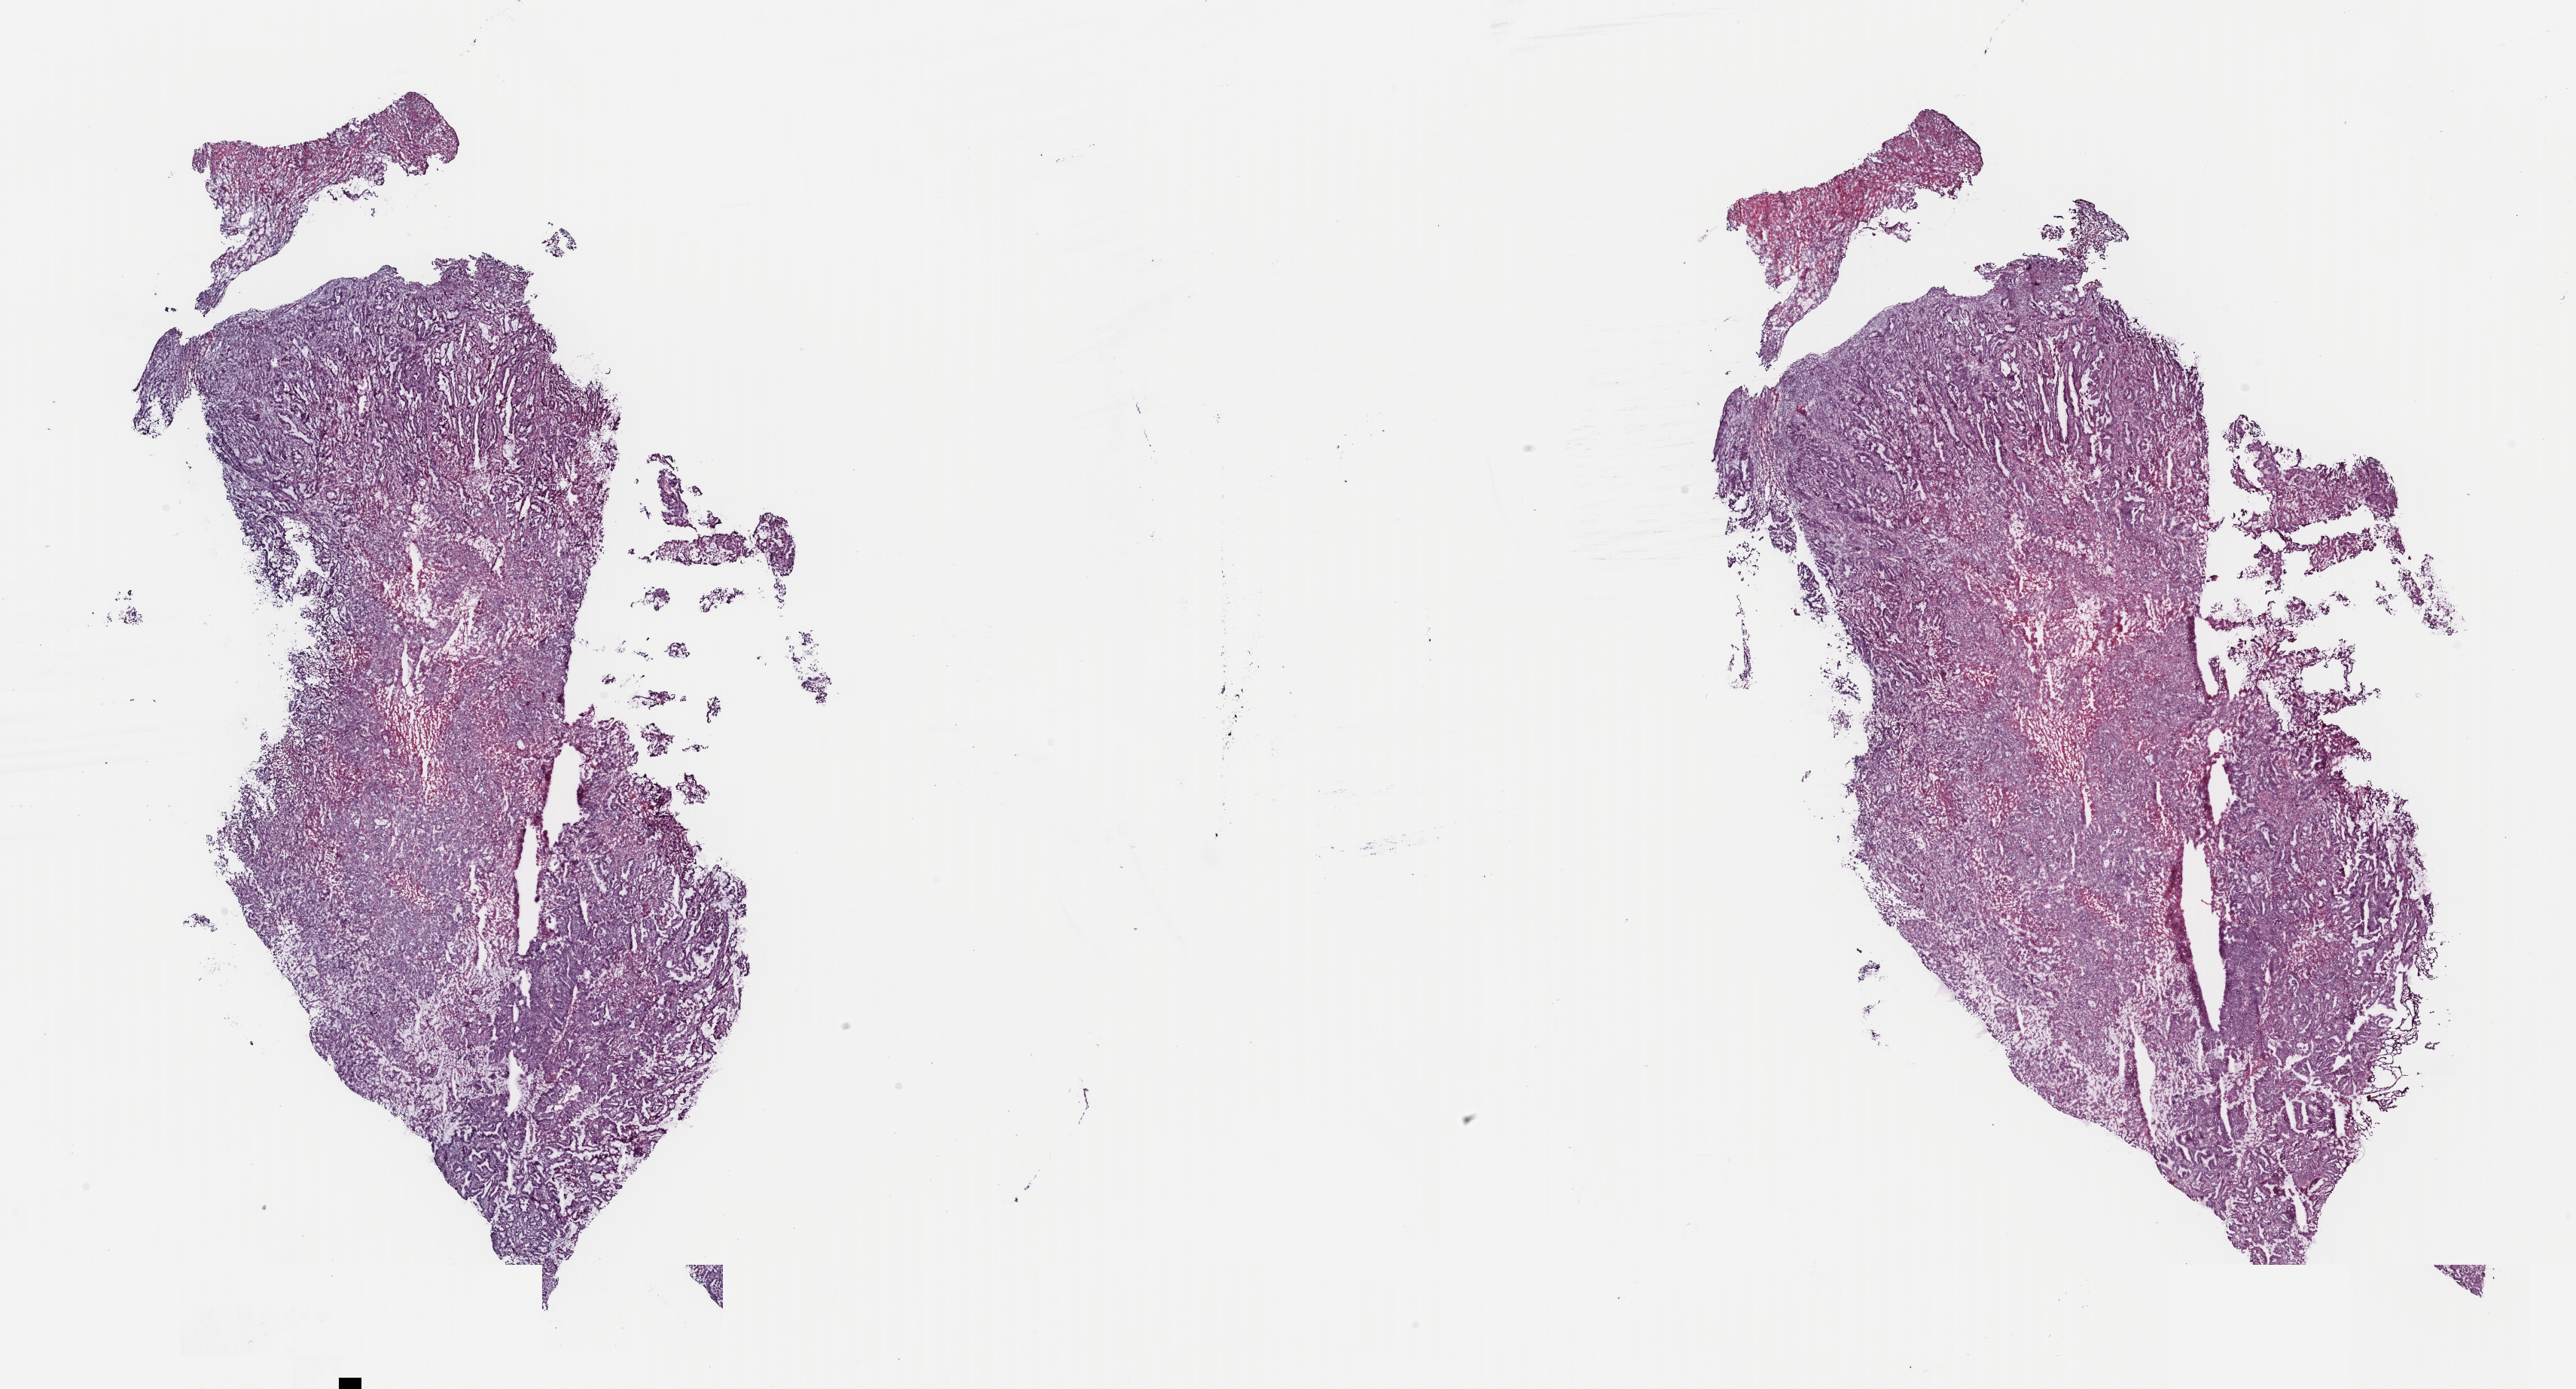
Whole-slide histology image, H&E-stained, shown as a low-resolution overview of the whole scanned area (about 27.0 x 14.6 mm, from a 40x scan), frozen section, primary tumour sample from the uterus. Female, age 83 years at initial diagnosis. Composition of this section per pathologist review: tumour cells 85%, tumour nuclei 80%, normal cells 0%, stromal cells 0%, necrosis 15%. Inflammatory infiltration, as recorded: lymphocyte infiltration 2%, monocyte infiltration 0%, neutrophil infiltration 0%.
Lymph nodes positive (case pathology): 0 of 12 examined. Histologic diagnosis: Mullerian mixed tumor (fundus uteri). FIGO stage: IB.